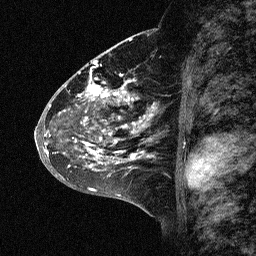
Breast MRI (dynamic contrast-enhanced), one sagittal slice. Position 30 of 64 along the scan axis. Dynamic contrast-enhanced study with each time point stored as its own series, time point 2 of 3 at this slice position (early post-contrast, ordered by acquisition time). 1.5 T. TE 4.5 ms, TR 11 ms. 2.06 mm slice thickness. 256 × 256 image matrix, field of view 200 × 200 mm. Patient: female, 46 years. From the clinical record (not read from this slice): setting: breast cancer imaged before/during neoadjuvant chemotherapy; receptor status: HER2-positive.
Annotated regions visible in this slice (semi-automatically segmented with operator editing):
- analysis volume of interest (the breast-tissue region the enhancement analysis was run in; not a lesion): bounding box <43,72,171,177> (left, top, right, bottom; pixels)
- tumour enhancement mask (voxels above the 90 % enhancement threshold inside the analysis volume of interest): <44,72,155,175>